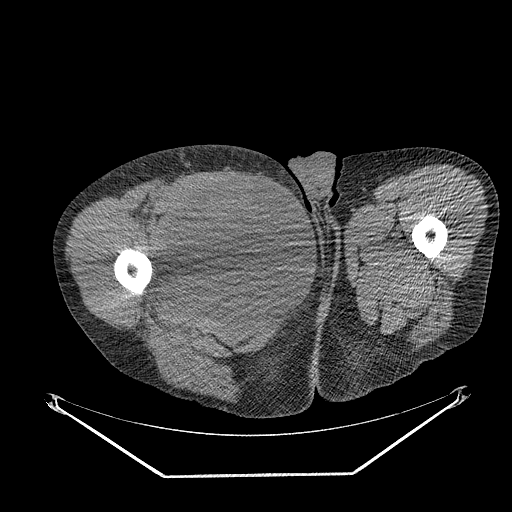
CT of an extremity soft-tissue mass (from a PET/CT study), one axial slice. 140 kVp. Soft-tissue window (W 400 / L 40 HU). 3.75 mm slice thickness. 512 × 512 image matrix, field of view 500 × 500 mm. Male patient. From the clinical record (not read from this slice): histological type: undifferentiated - pleiomorphic; grade: high; site of the primary tumour: right thigh.
Structures marked on this image (expert contour drawn on MRI and transferred to this co-registered scan by the dataset authors):
- gross tumour volume including surrounding oedema: bounding box <160,176,268,280> (left, top, right, bottom; pixels)
- gross tumour volume (mass): <160,176,268,280>